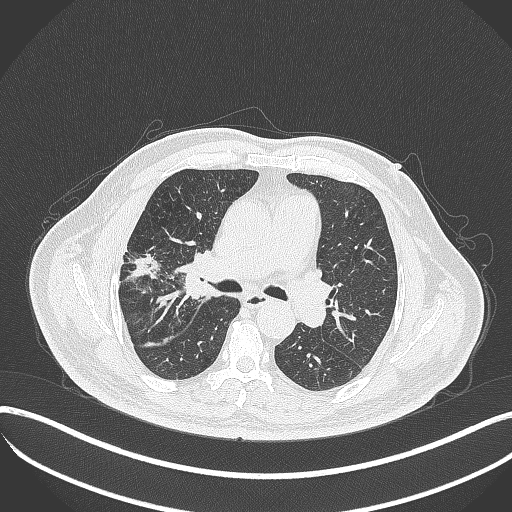
Chest CT, one axial slice; slice 217 of 401 in the series (ordered by position); lung window (W 1500 / L -600 HU); 1 mm slice thickness; 512 × 512 image matrix, field of view 400 × 400 mm. Patient: male, 72 years. From the clinical record (not read from this slice): clinical TNM (as recorded): T1c N0 M0.
Outlined on this slice (bounding box drawn by a radiologist):
- lung tumour (recorded histology: squamous cell carcinoma): bounding box [x1, y1, x2, y2] px = [165, 247, 204, 305]